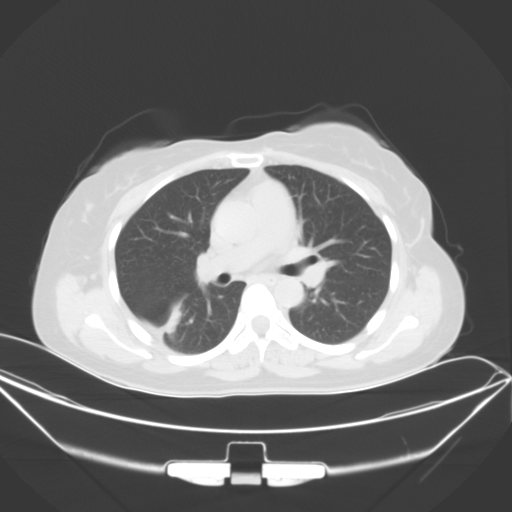
Chest CT, one axial slice; position 24 of 46 along the scan axis; 120 kVp; lung window (W 1500 / L -600 HU); 5 mm slice thickness; 512 × 512 image matrix, field of view 407 × 407 mm. Female patient, age 42 years. Case-level facts recorded for this patient, not image findings: clinical TNM (as recorded): T1c N0 M1a.
Annotated regions visible in this slice (bounding box drawn by a radiologist):
- lung tumour (recorded histology: adenocarcinoma): bounding box (x1, y1, x2, y2) in pixels: (157, 288, 197, 338)